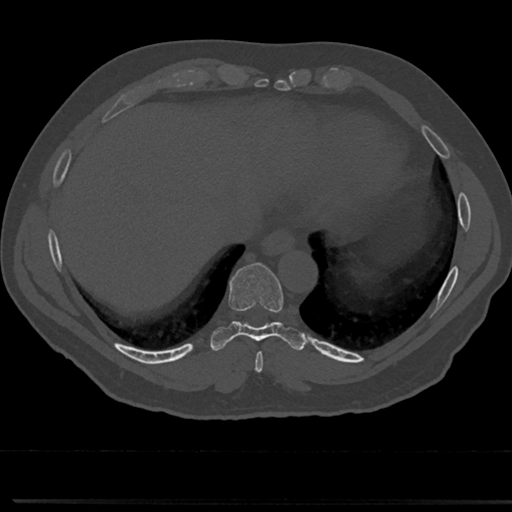
CT including the spine, one axial slice; slice 305 of 817 in the series (ordered by position); reconstruction kernel Br40s/3; 120 kVp; bone window (W 1800 / L 400 HU); 0.5 mm slice thickness; 512 × 512 image matrix, field of view 355 × 355 mm. Patient: male, 61 years. From the clinical record (not read from this slice): primary cancer: prostate.
Structures marked on this image (semi-automatic segmentation, software-assisted and operator-edited):
- T8 vertebra: bounding box (x1, y1, x2, y2) in pixels: (232, 304, 287, 355)
- T9 vertebra: (232, 266, 283, 329)